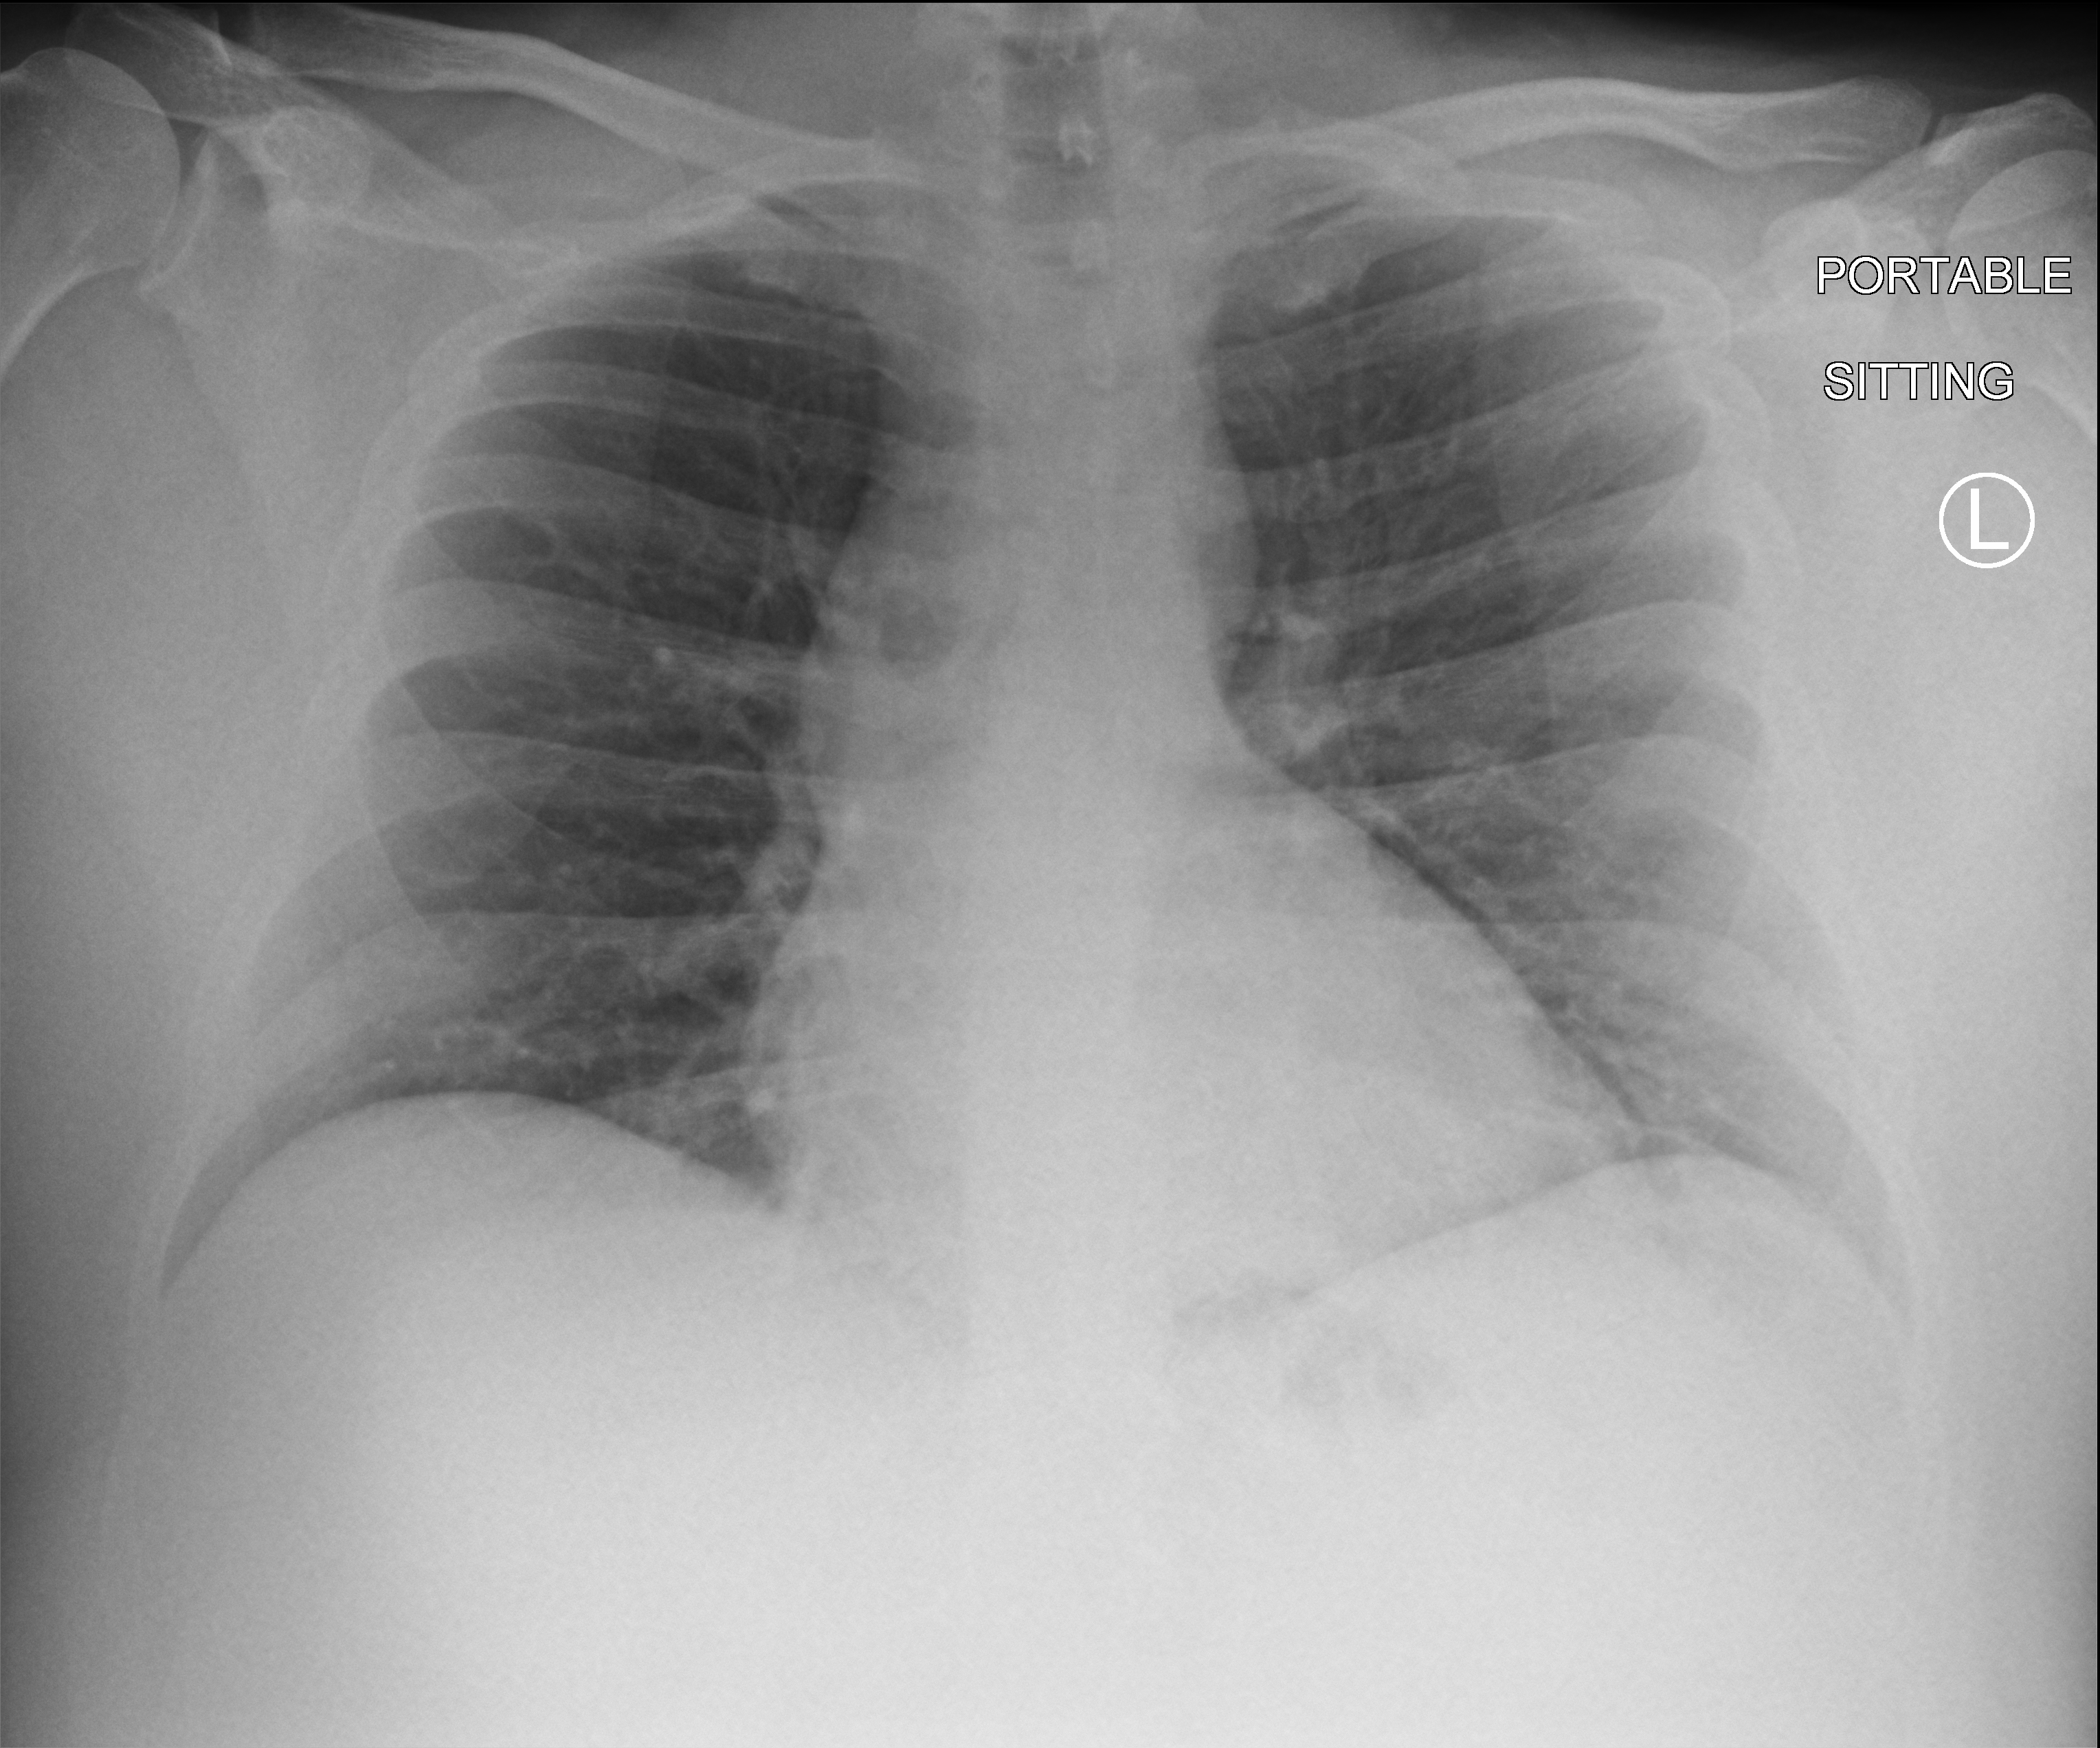
Chest X-ray (portable); anteroposterior (AP) projection. Patient hospitalised with COVID-19; male, aged 18–59 years.
Hospital-stay facts (about this admission, not read from this image; timing relative to this image not recorded): admitted to intensive care during this hospital stay: no; mechanically ventilated during this hospital stay: no.